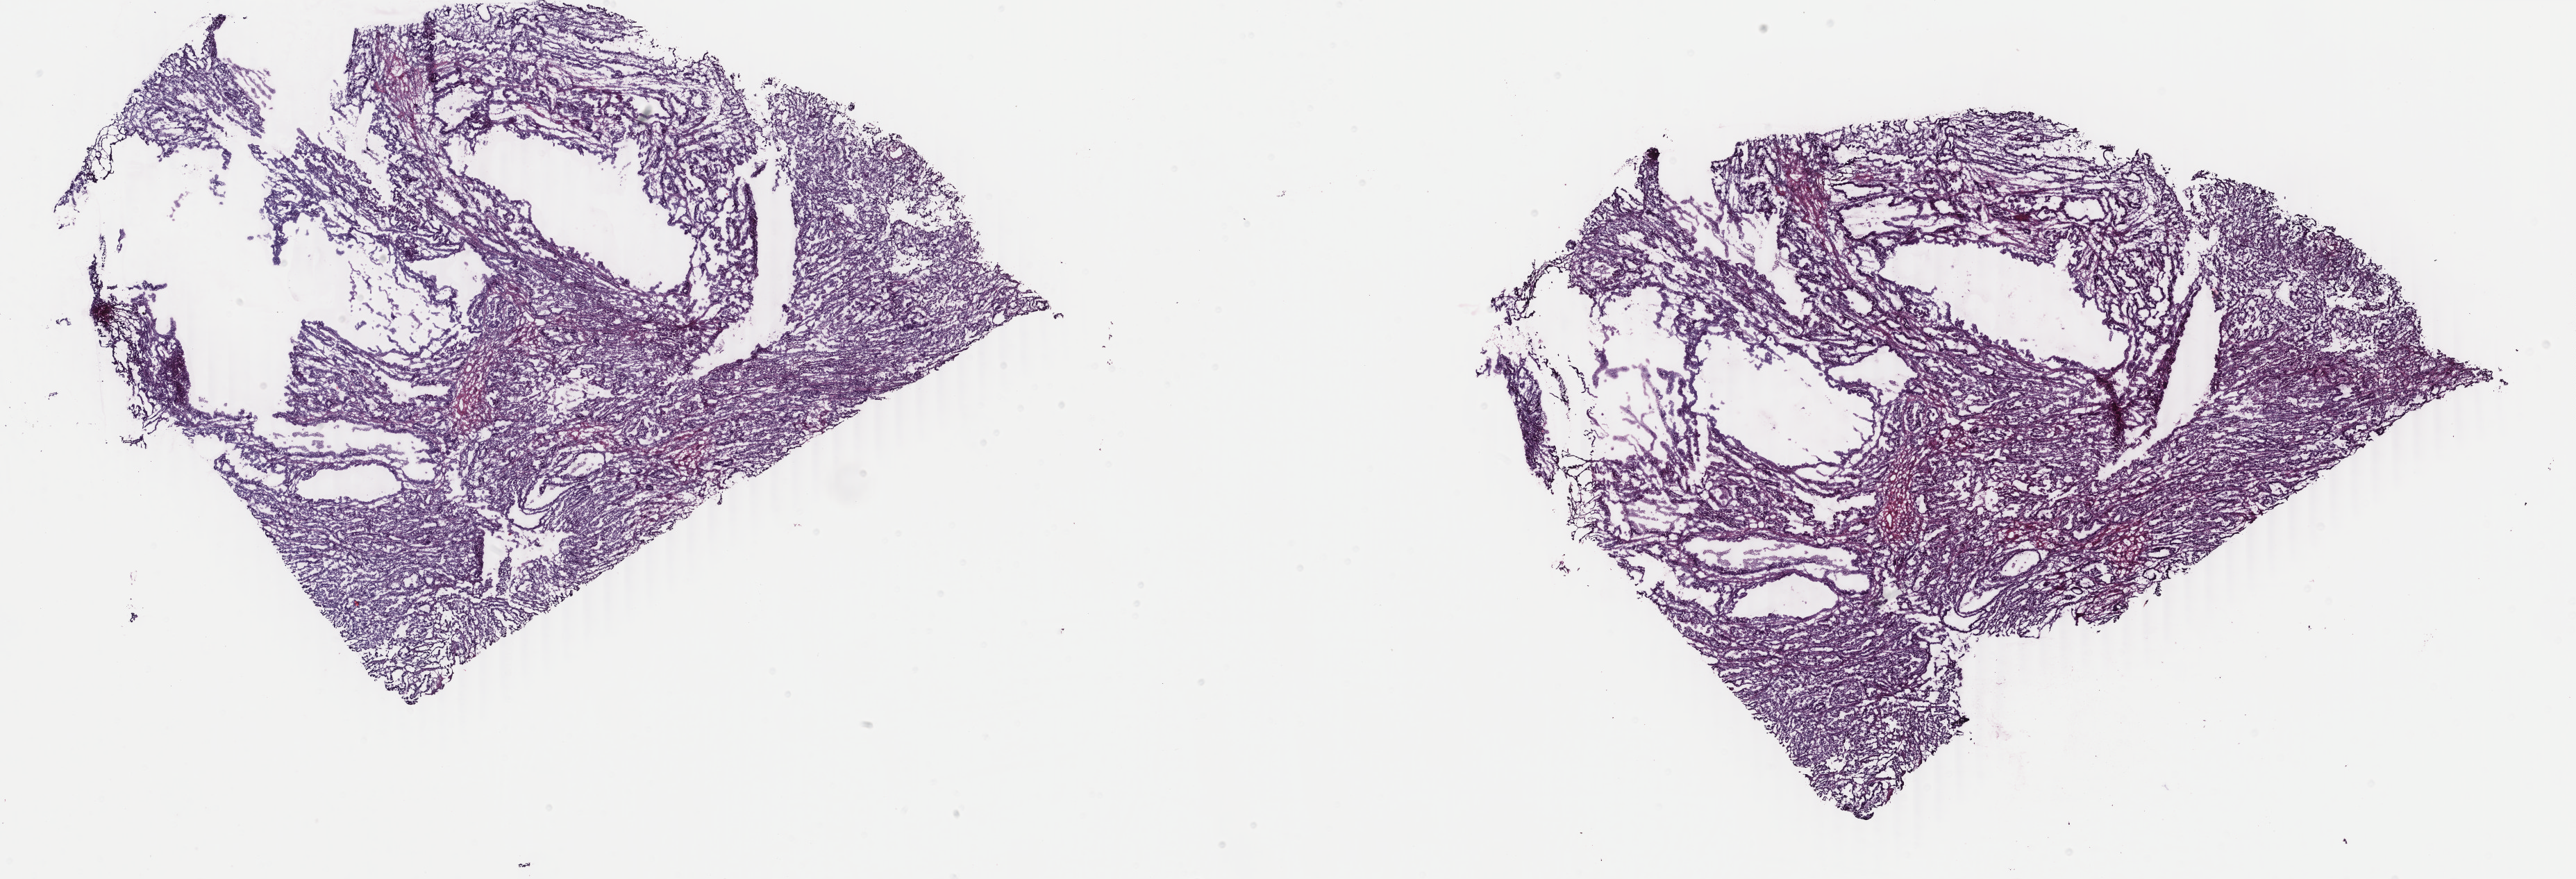
H&E whole-slide image — shown as a low-resolution overview of the whole scanned area (about 29.5 x 10.1 mm, from a 40x scan). Frozen section from the bottom of the tissue portion. Sample: primary tumour, uterus. Female patient; age at initial diagnosis 42 years. Histologic grade: G1 (well differentiated). Slide review estimates, as recorded: tumour cells 100%, tumour nuclei 75%, normal cells 0%, stromal cells 0%, necrosis 0%. Inflammatory infiltration, as recorded: lymphocyte infiltration 0%, monocyte infiltration 0%, neutrophil infiltration 0%.
FIGO stage: IA. Pathologic diagnosis: Endometrioid adenocarcinoma, NOS (endometrium). Lymph nodes positive (case pathology): 0 of 14 examined.